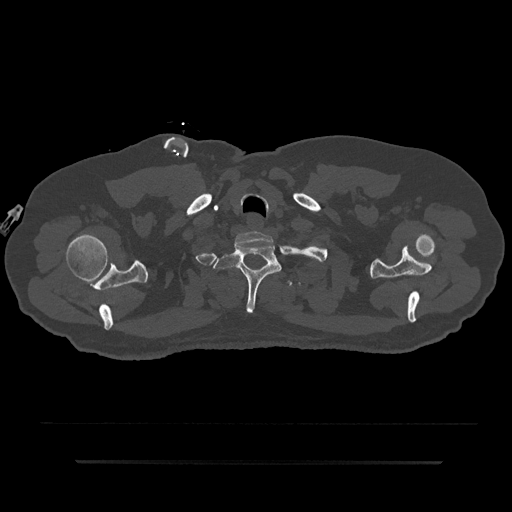
CT including the spine, one axial slice. Slice 739 of 797 in the series (ordered by position). Reconstruction kernel Br40s/3. Bone window (W 1800 / L 400 HU). 0.5 mm slice thickness. 512 × 512 image matrix, field of view 464 × 464 mm. Male patient, age 59 years. From the clinical record (not read from this slice): primary cancer: bile ducts; vertebrae with lytic lesions (as recorded): T10.
Structures marked on this image (semi-automatic segmentation, software-assisted and operator-edited):
- T1 vertebra: bounding box [x1, y1, x2, y2] px = [213, 245, 282, 313]
- T2 vertebra: [286, 280, 293, 286]